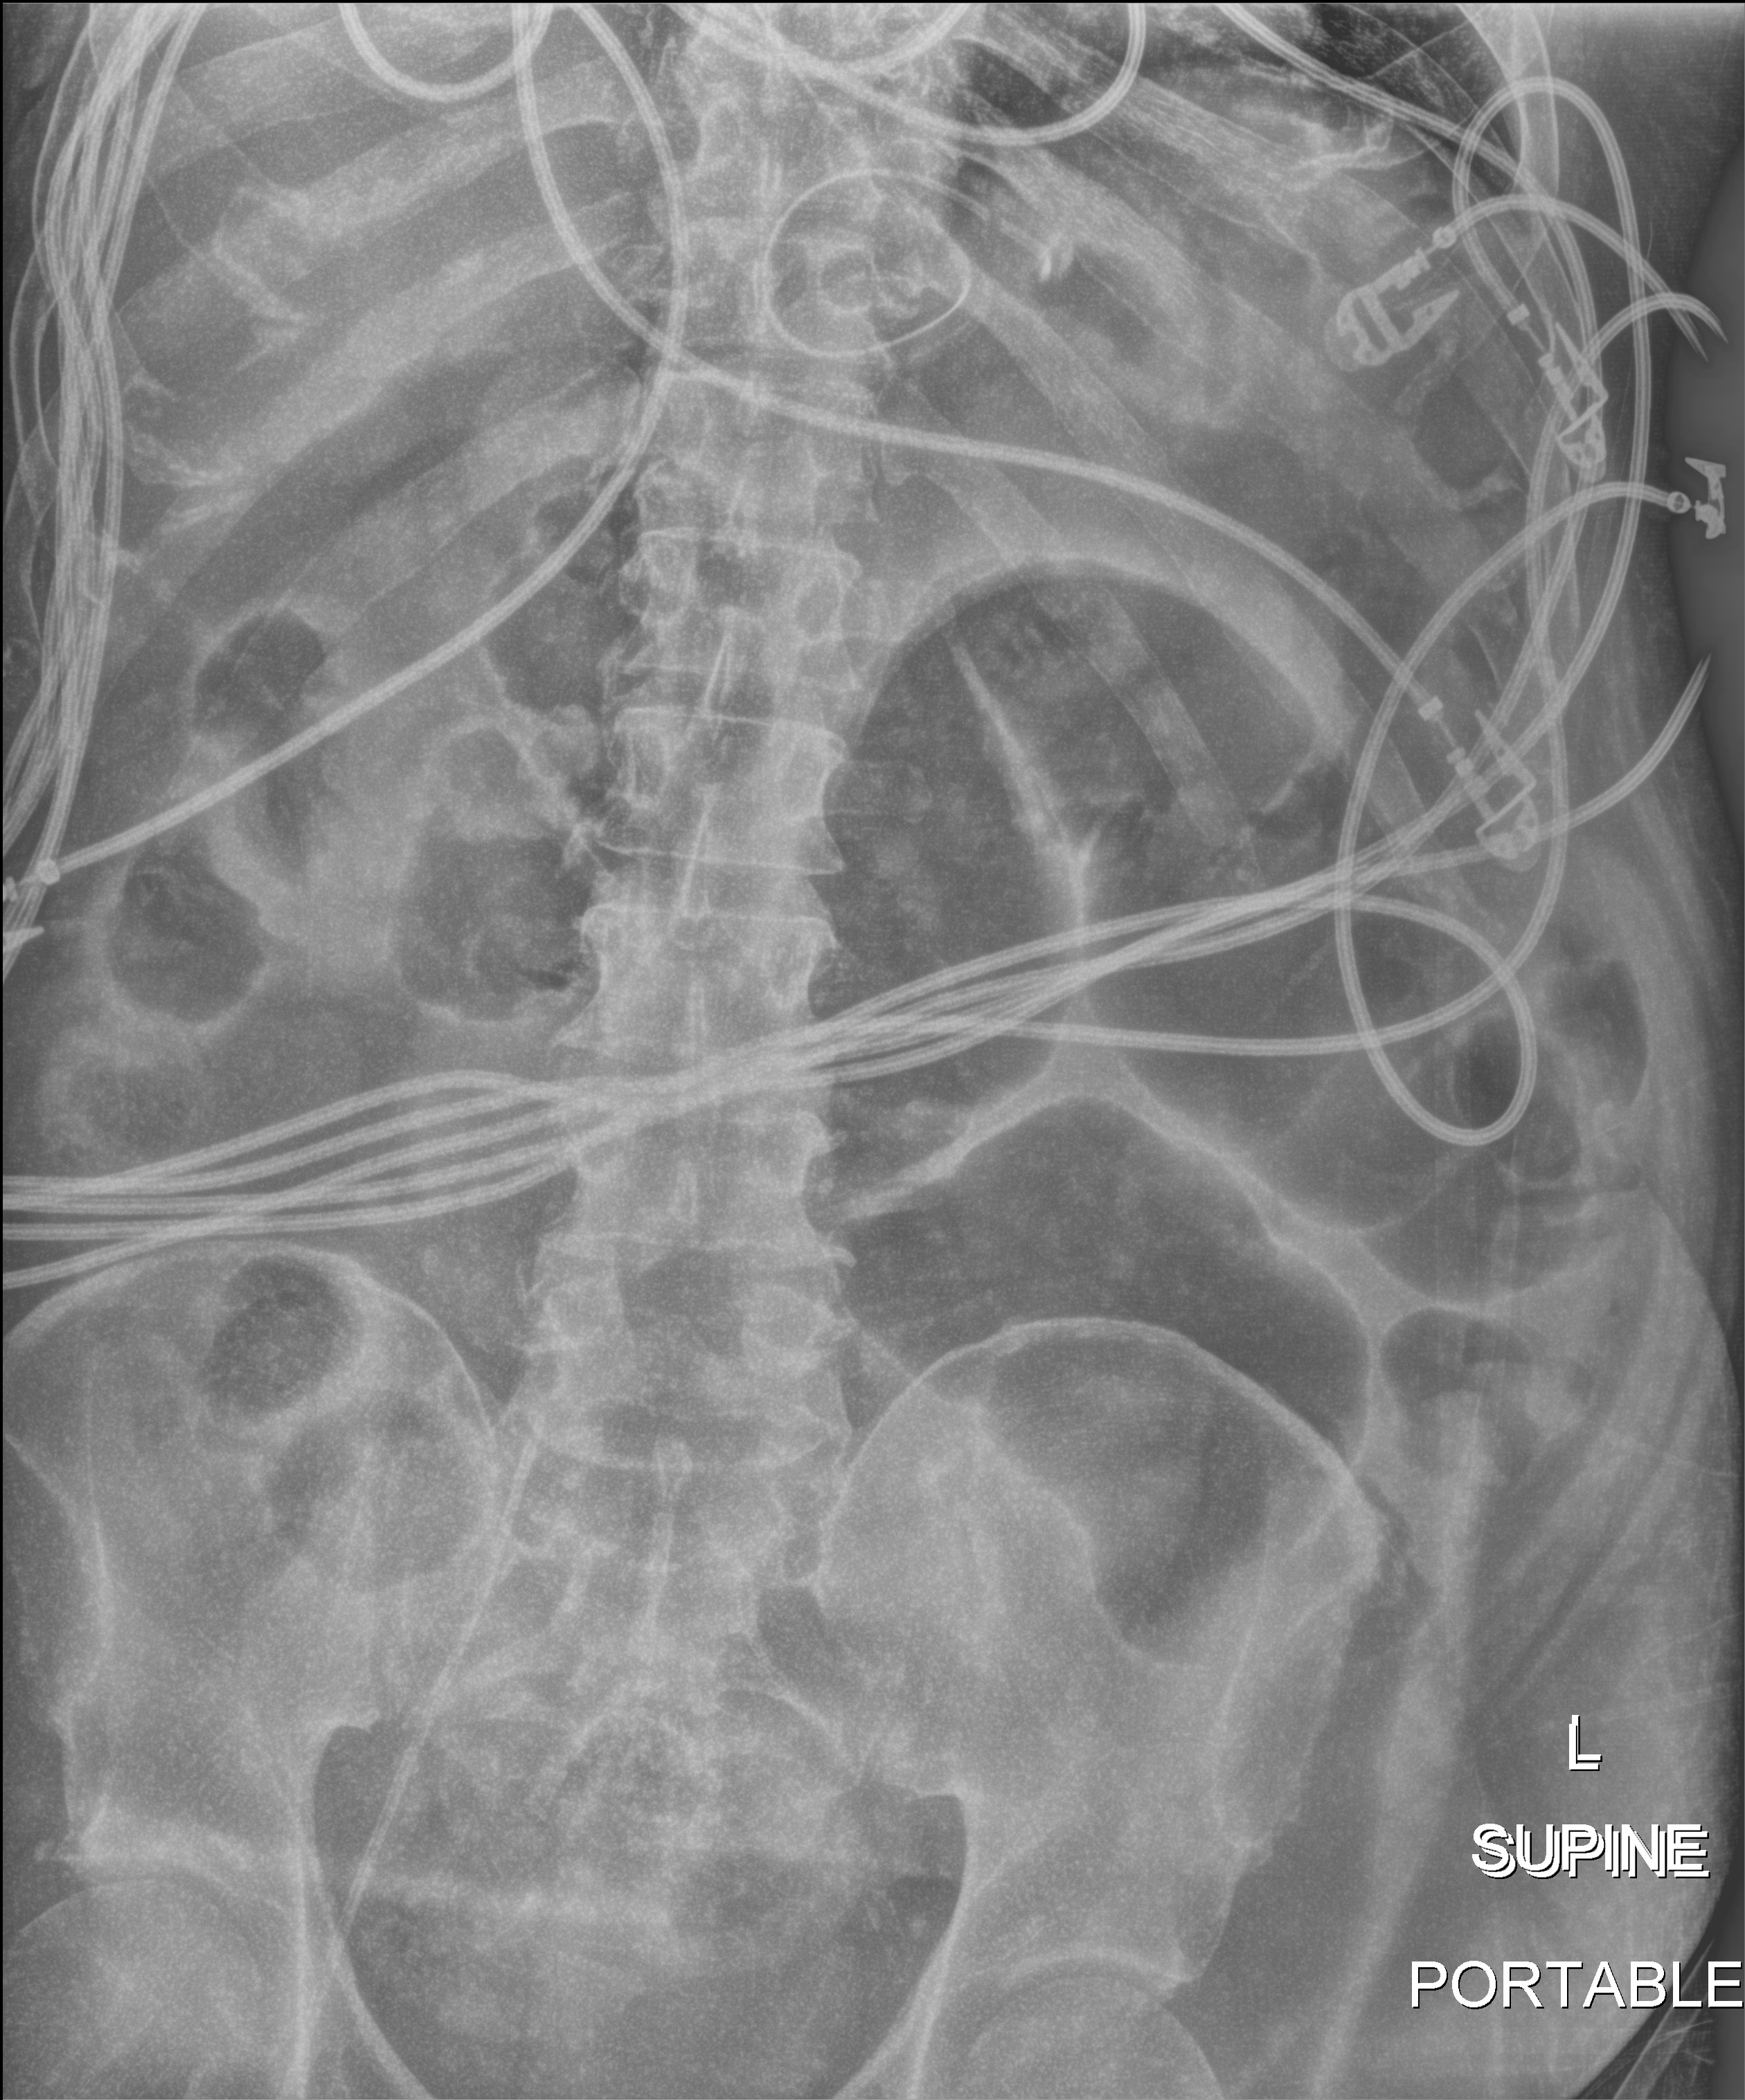
Abdomen X-ray (portable). Patient hospitalised with COVID-19, aged 18–59 years.
Admission-level facts for this patient (not findings on this image; timing relative to this image not recorded): COPD (admission record): no.